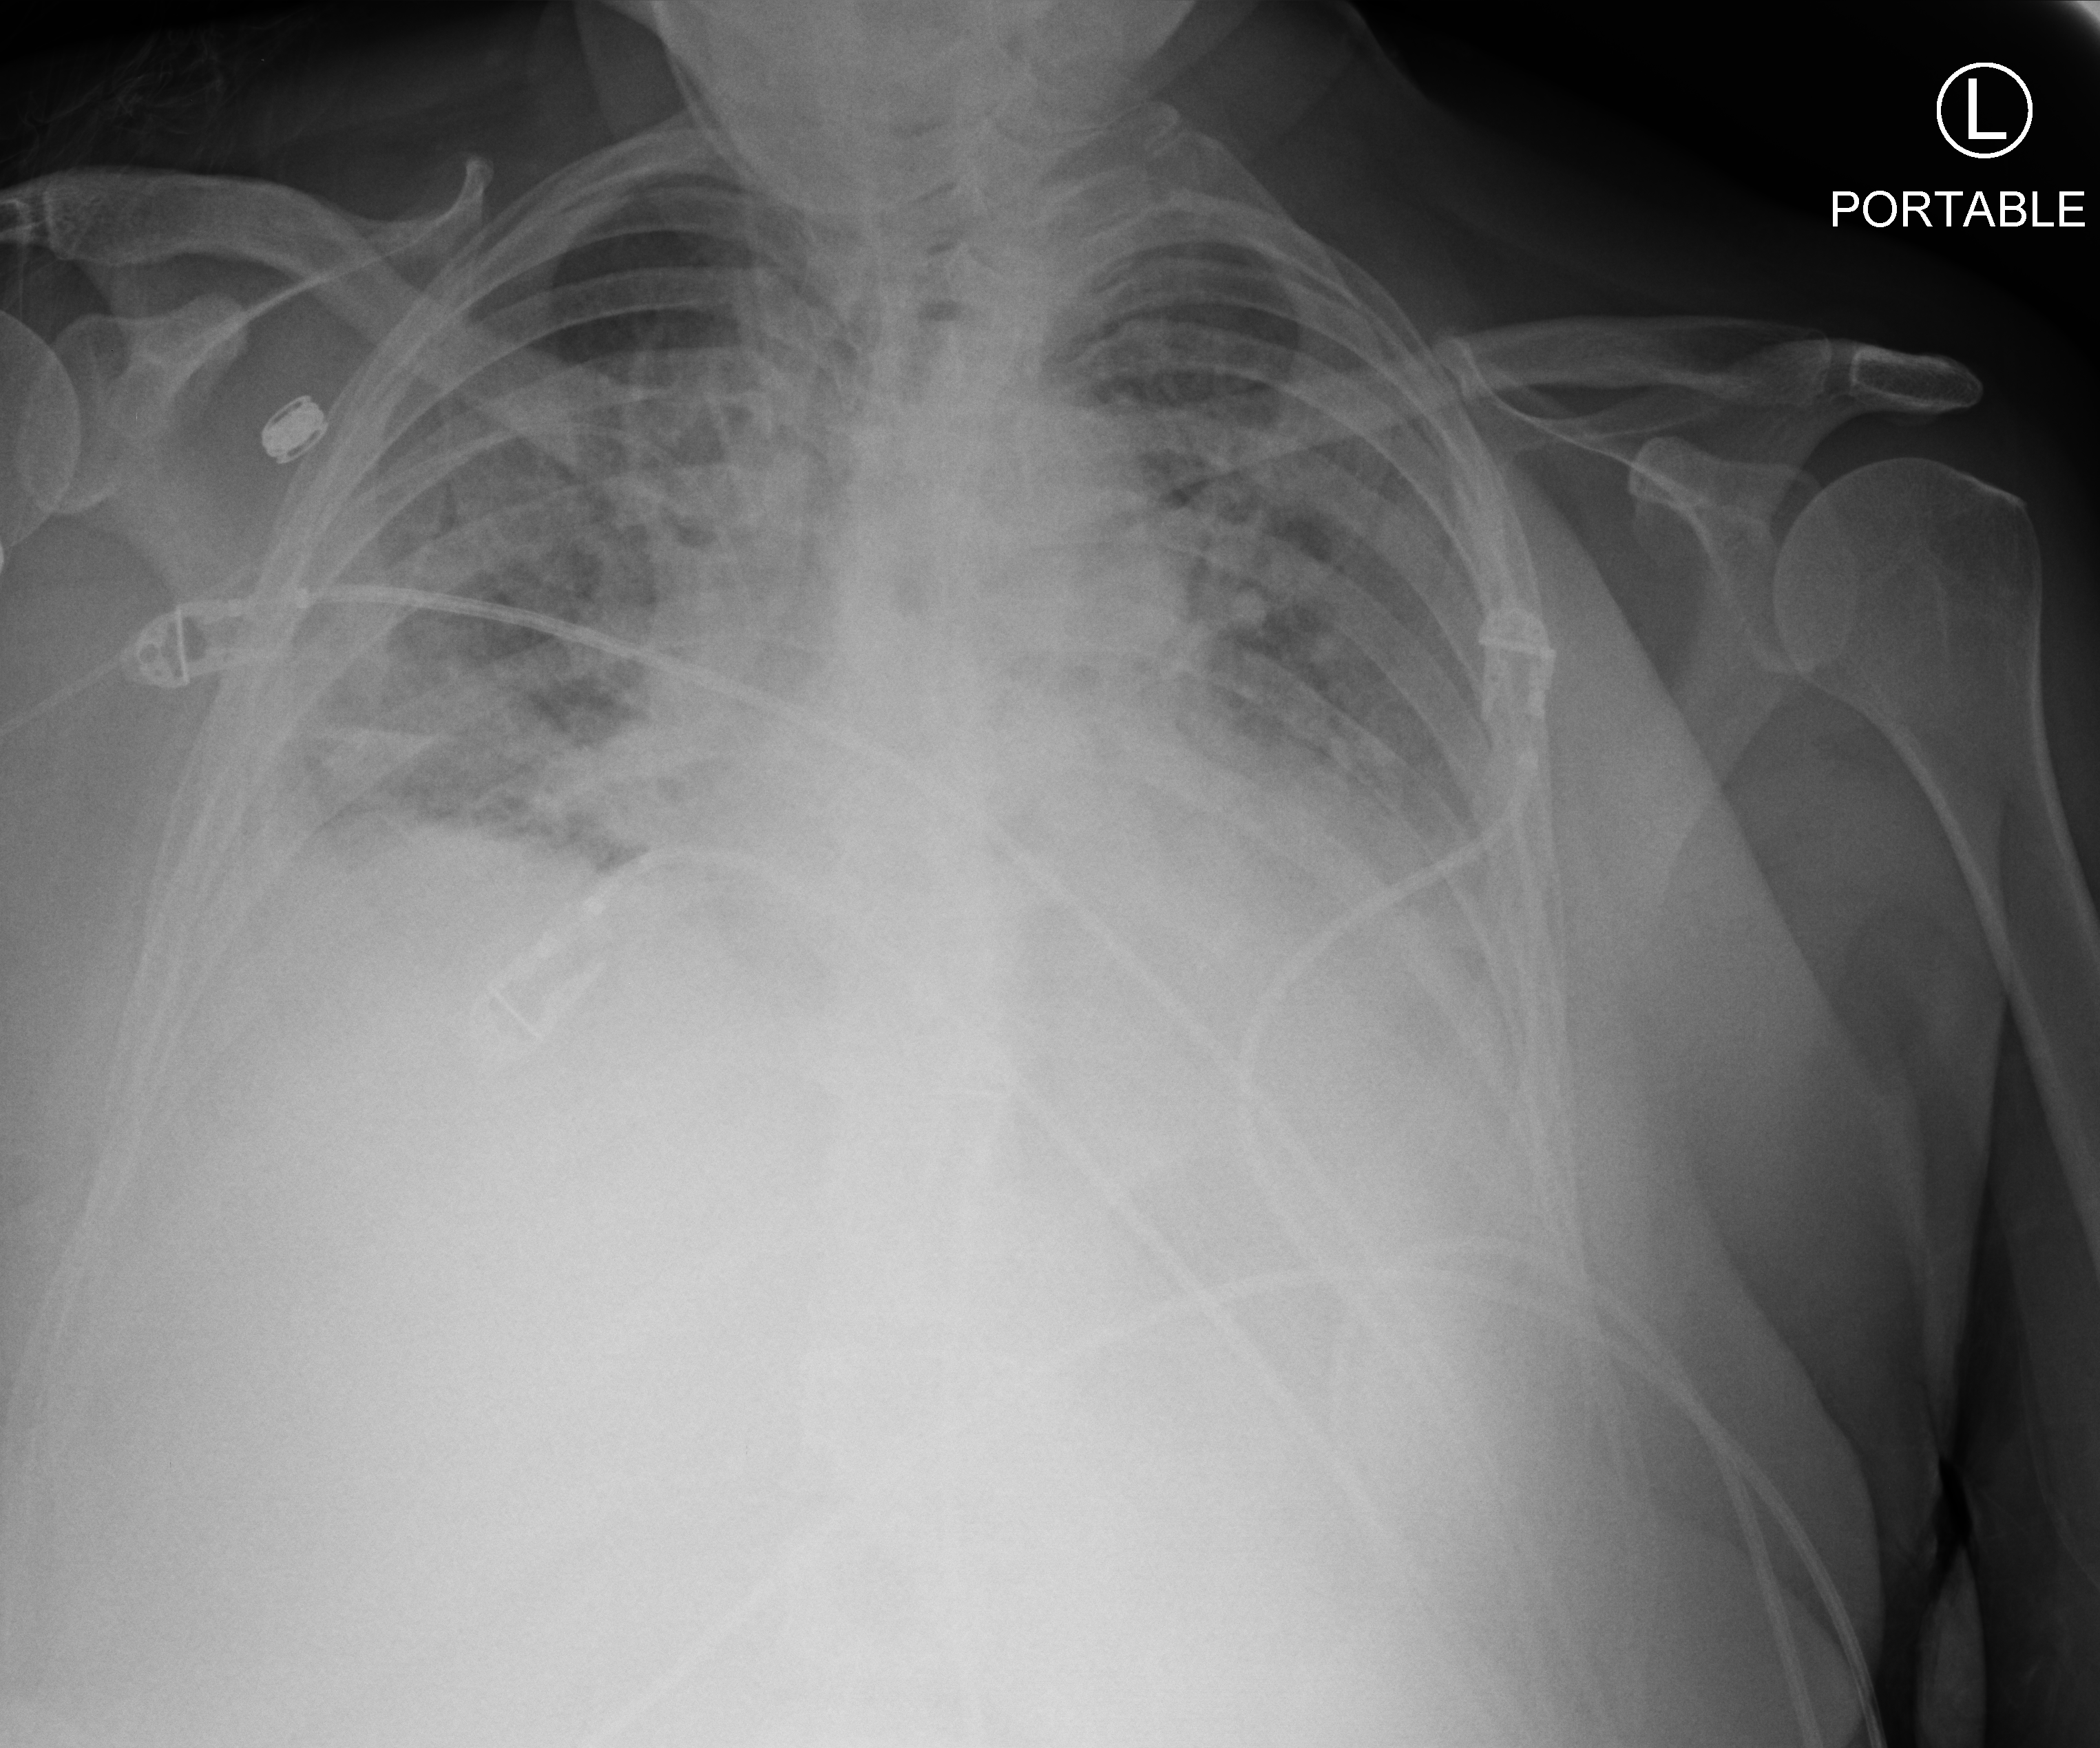
Bedside chest radiograph (computed radiography); anteroposterior (AP) projection. Patient hospitalised with COVID-19; female, aged 60–74 years.
Admission-level facts for this patient (not findings on this image; timing relative to this image not recorded):
- length of hospital stay: 50 days
- mechanically ventilated during this hospital stay: yes